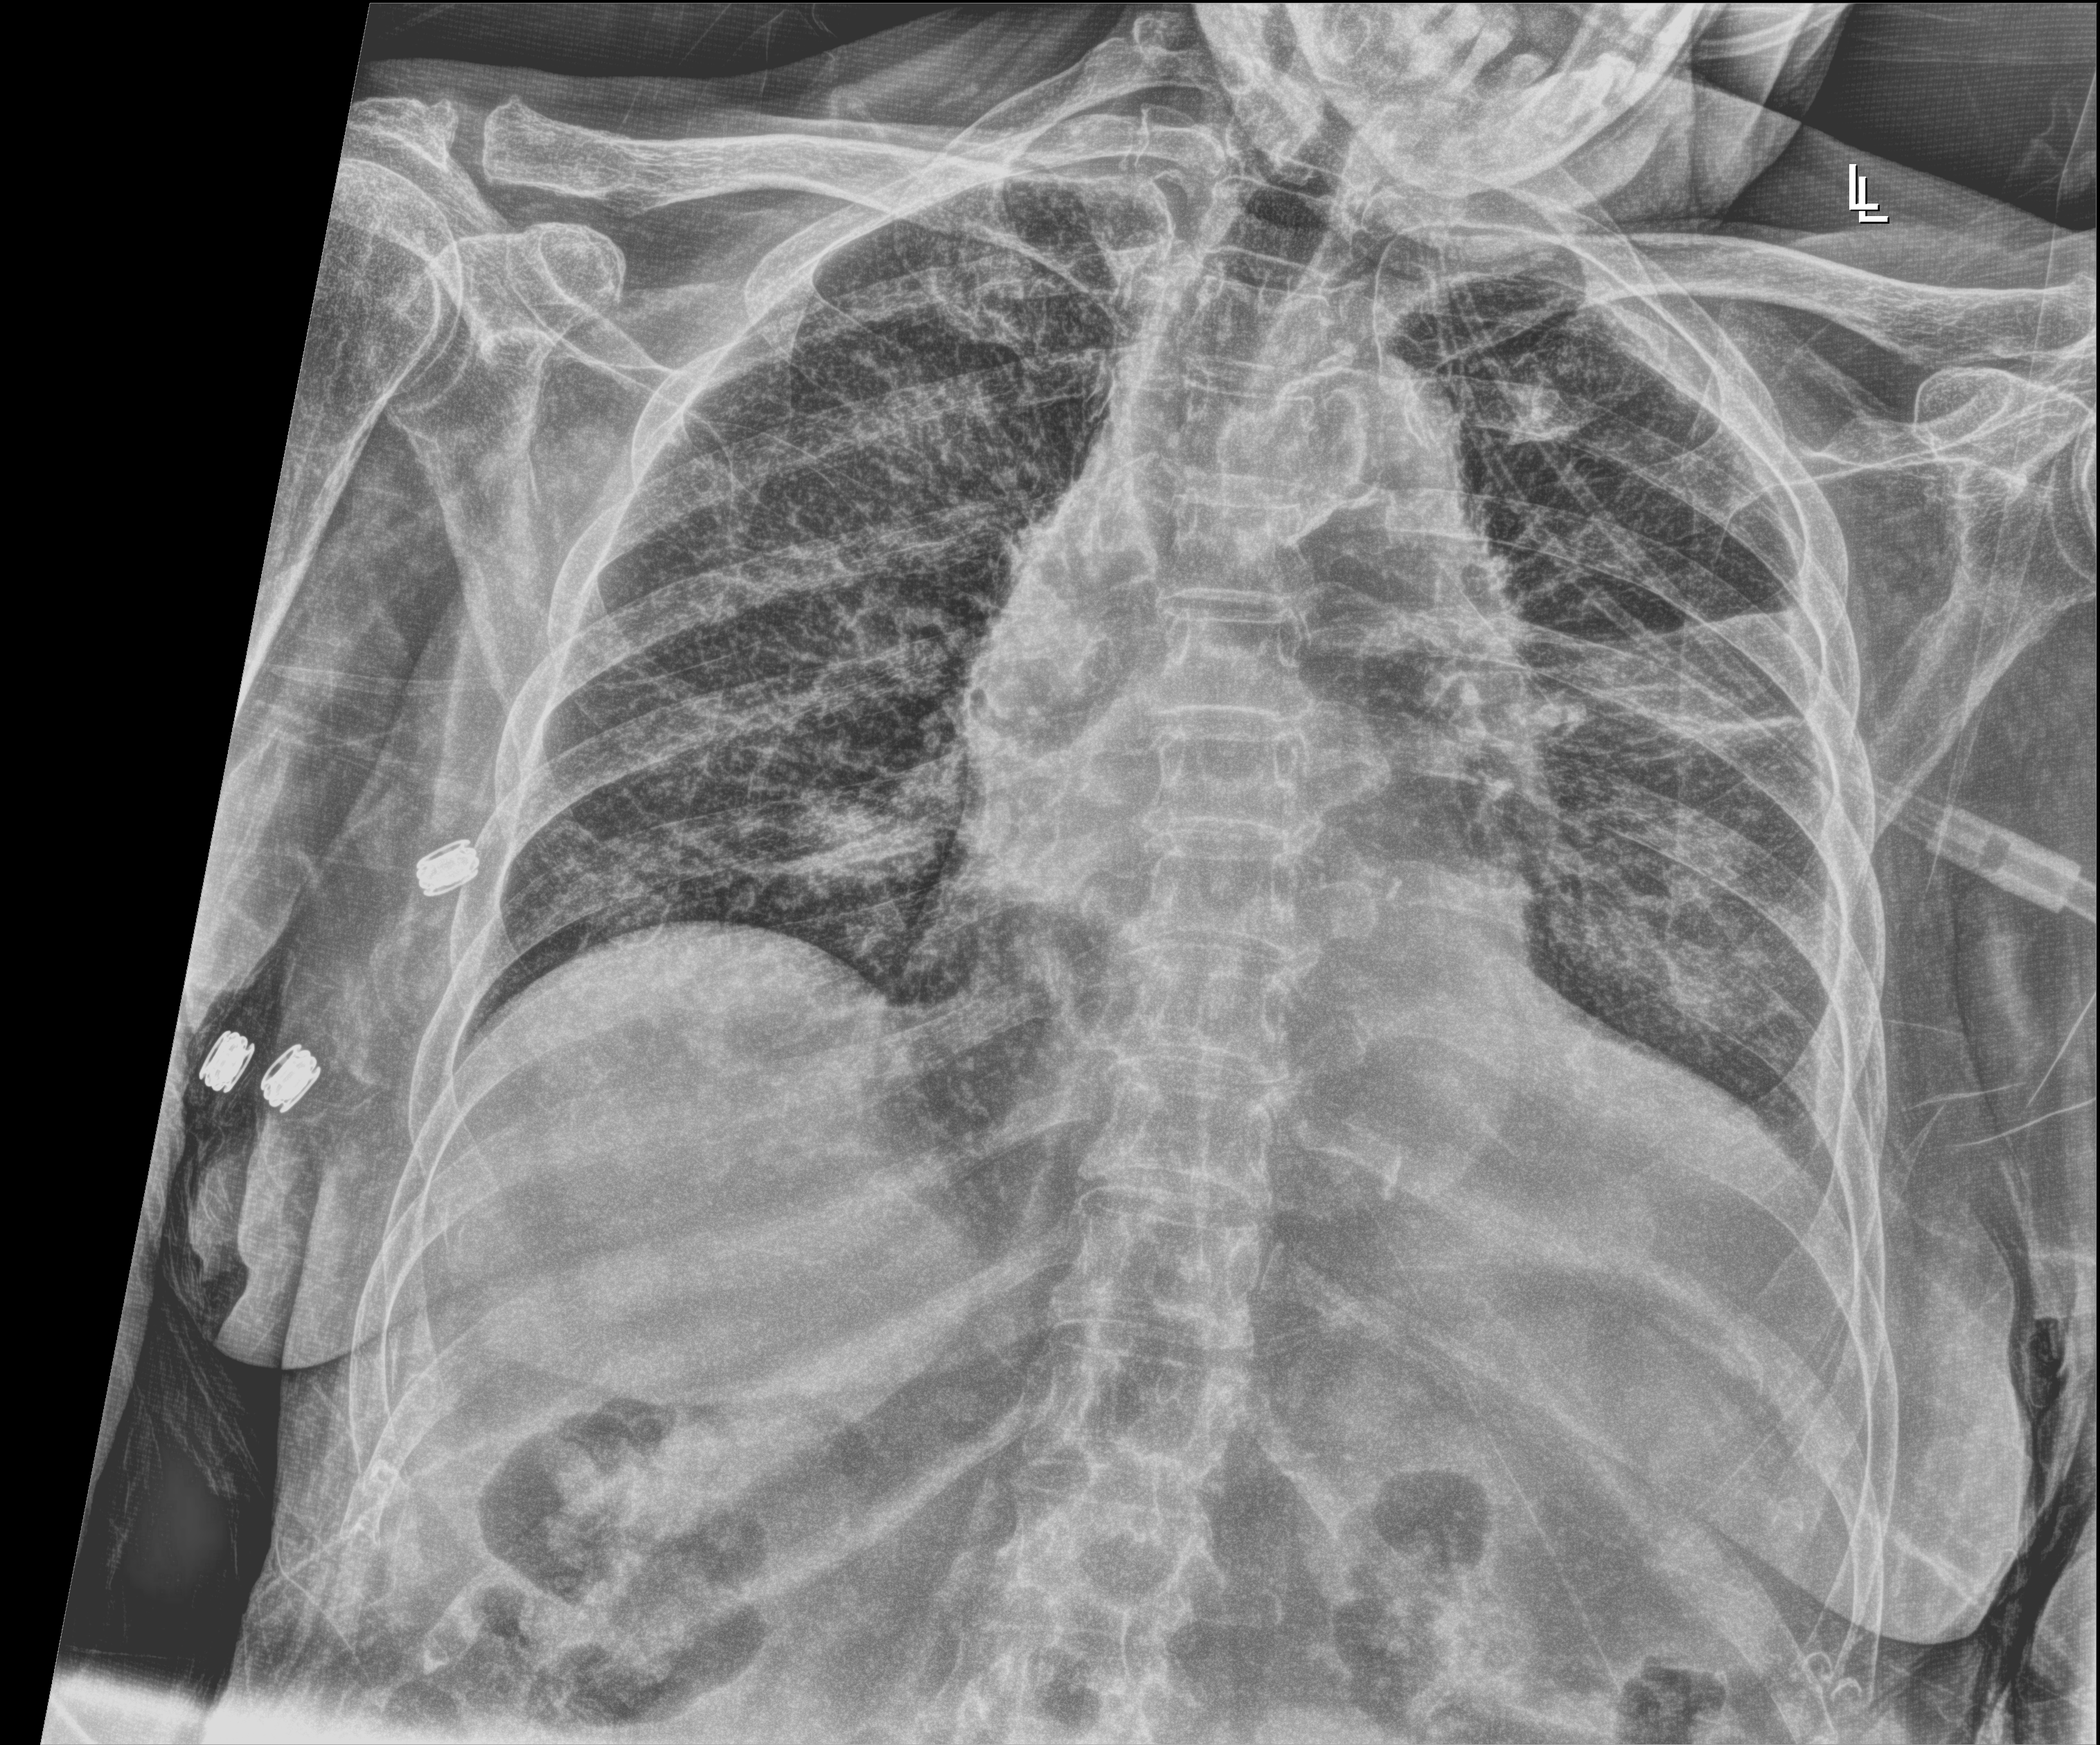
Chest radiograph (digital radiography); anteroposterior (AP) projection. Patient hospitalised with COVID-19; female, aged 75–90 years.
From the hospital-stay record, not from the radiograph (when in the stay this image was taken is not recorded):
- length of hospital stay: 8 days
- mechanically ventilated during this hospital stay: no
- admitted to intensive care during this hospital stay: no